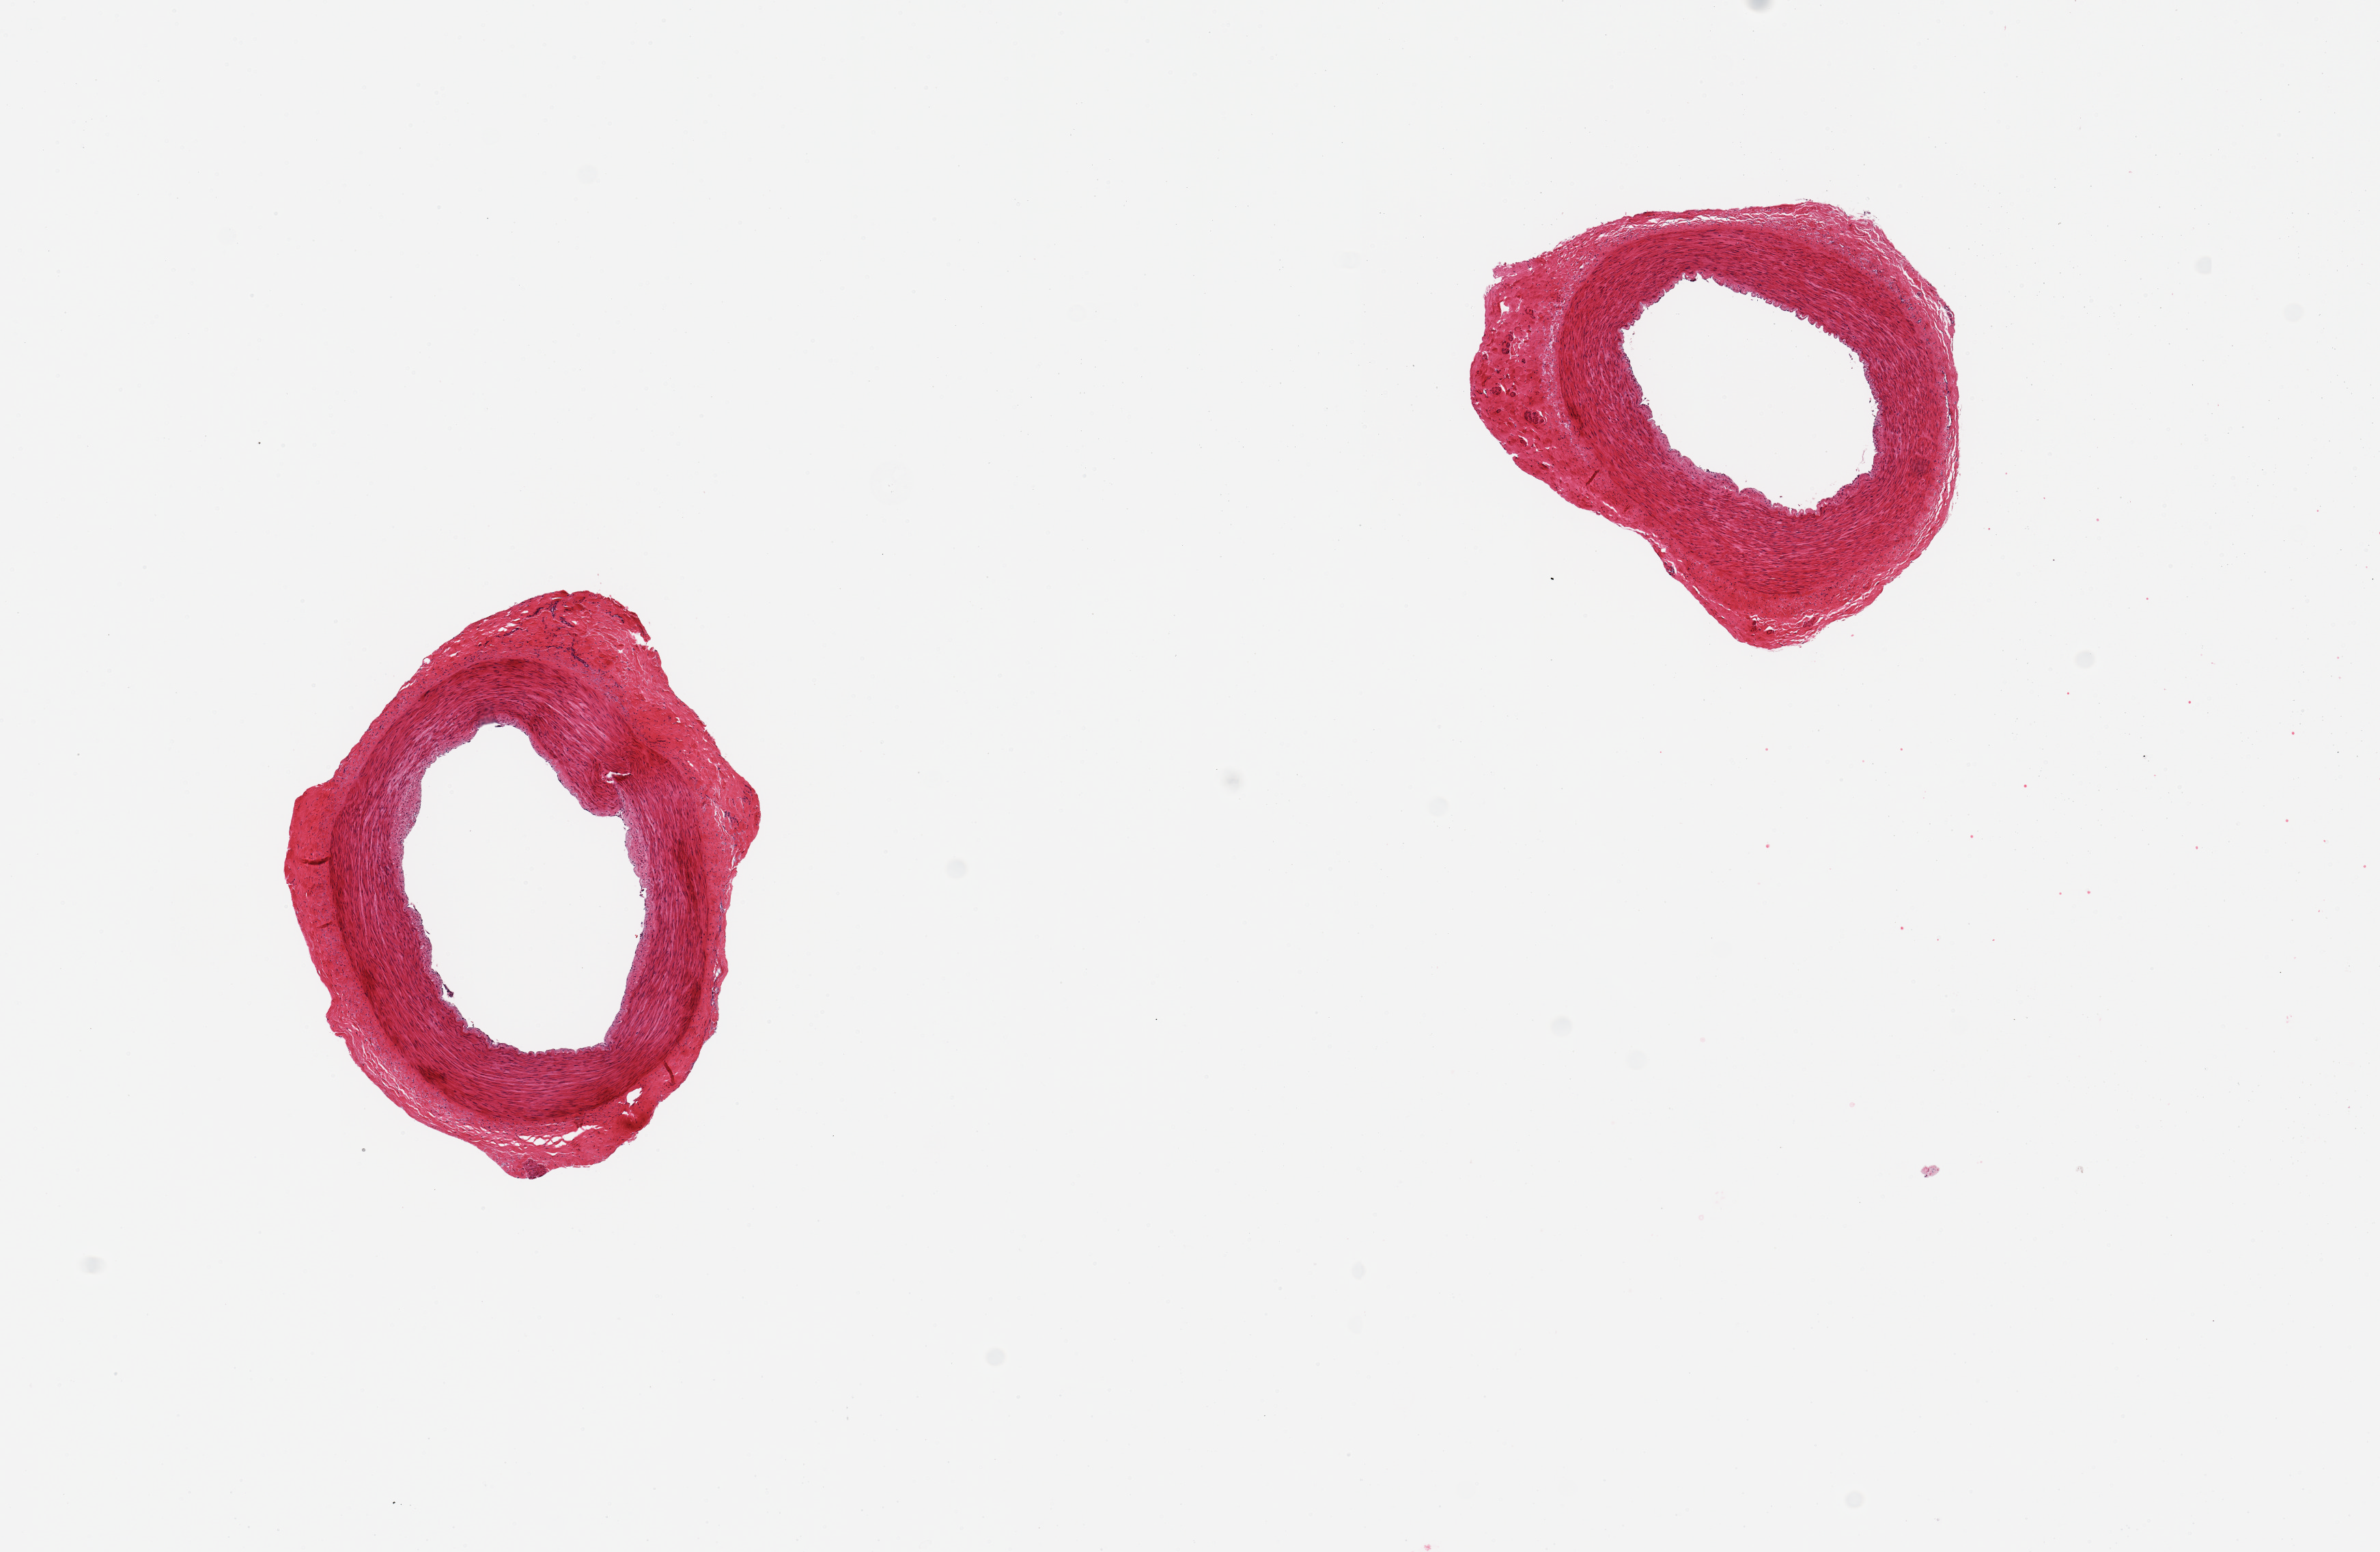
Digitized haematoxylin and eosin-stained section — shown as a low-resolution overview of the whole scanned area (about 13.8 x 9.0 mm, from a 20x scan), PAXgene-fixed paraffin-embedded (PFPE) section, target tissue: tibial artery, donor tissue sample. Donor sex: male.
Reviewer comment on this tissue sample: 2 pieces; well trimmed.